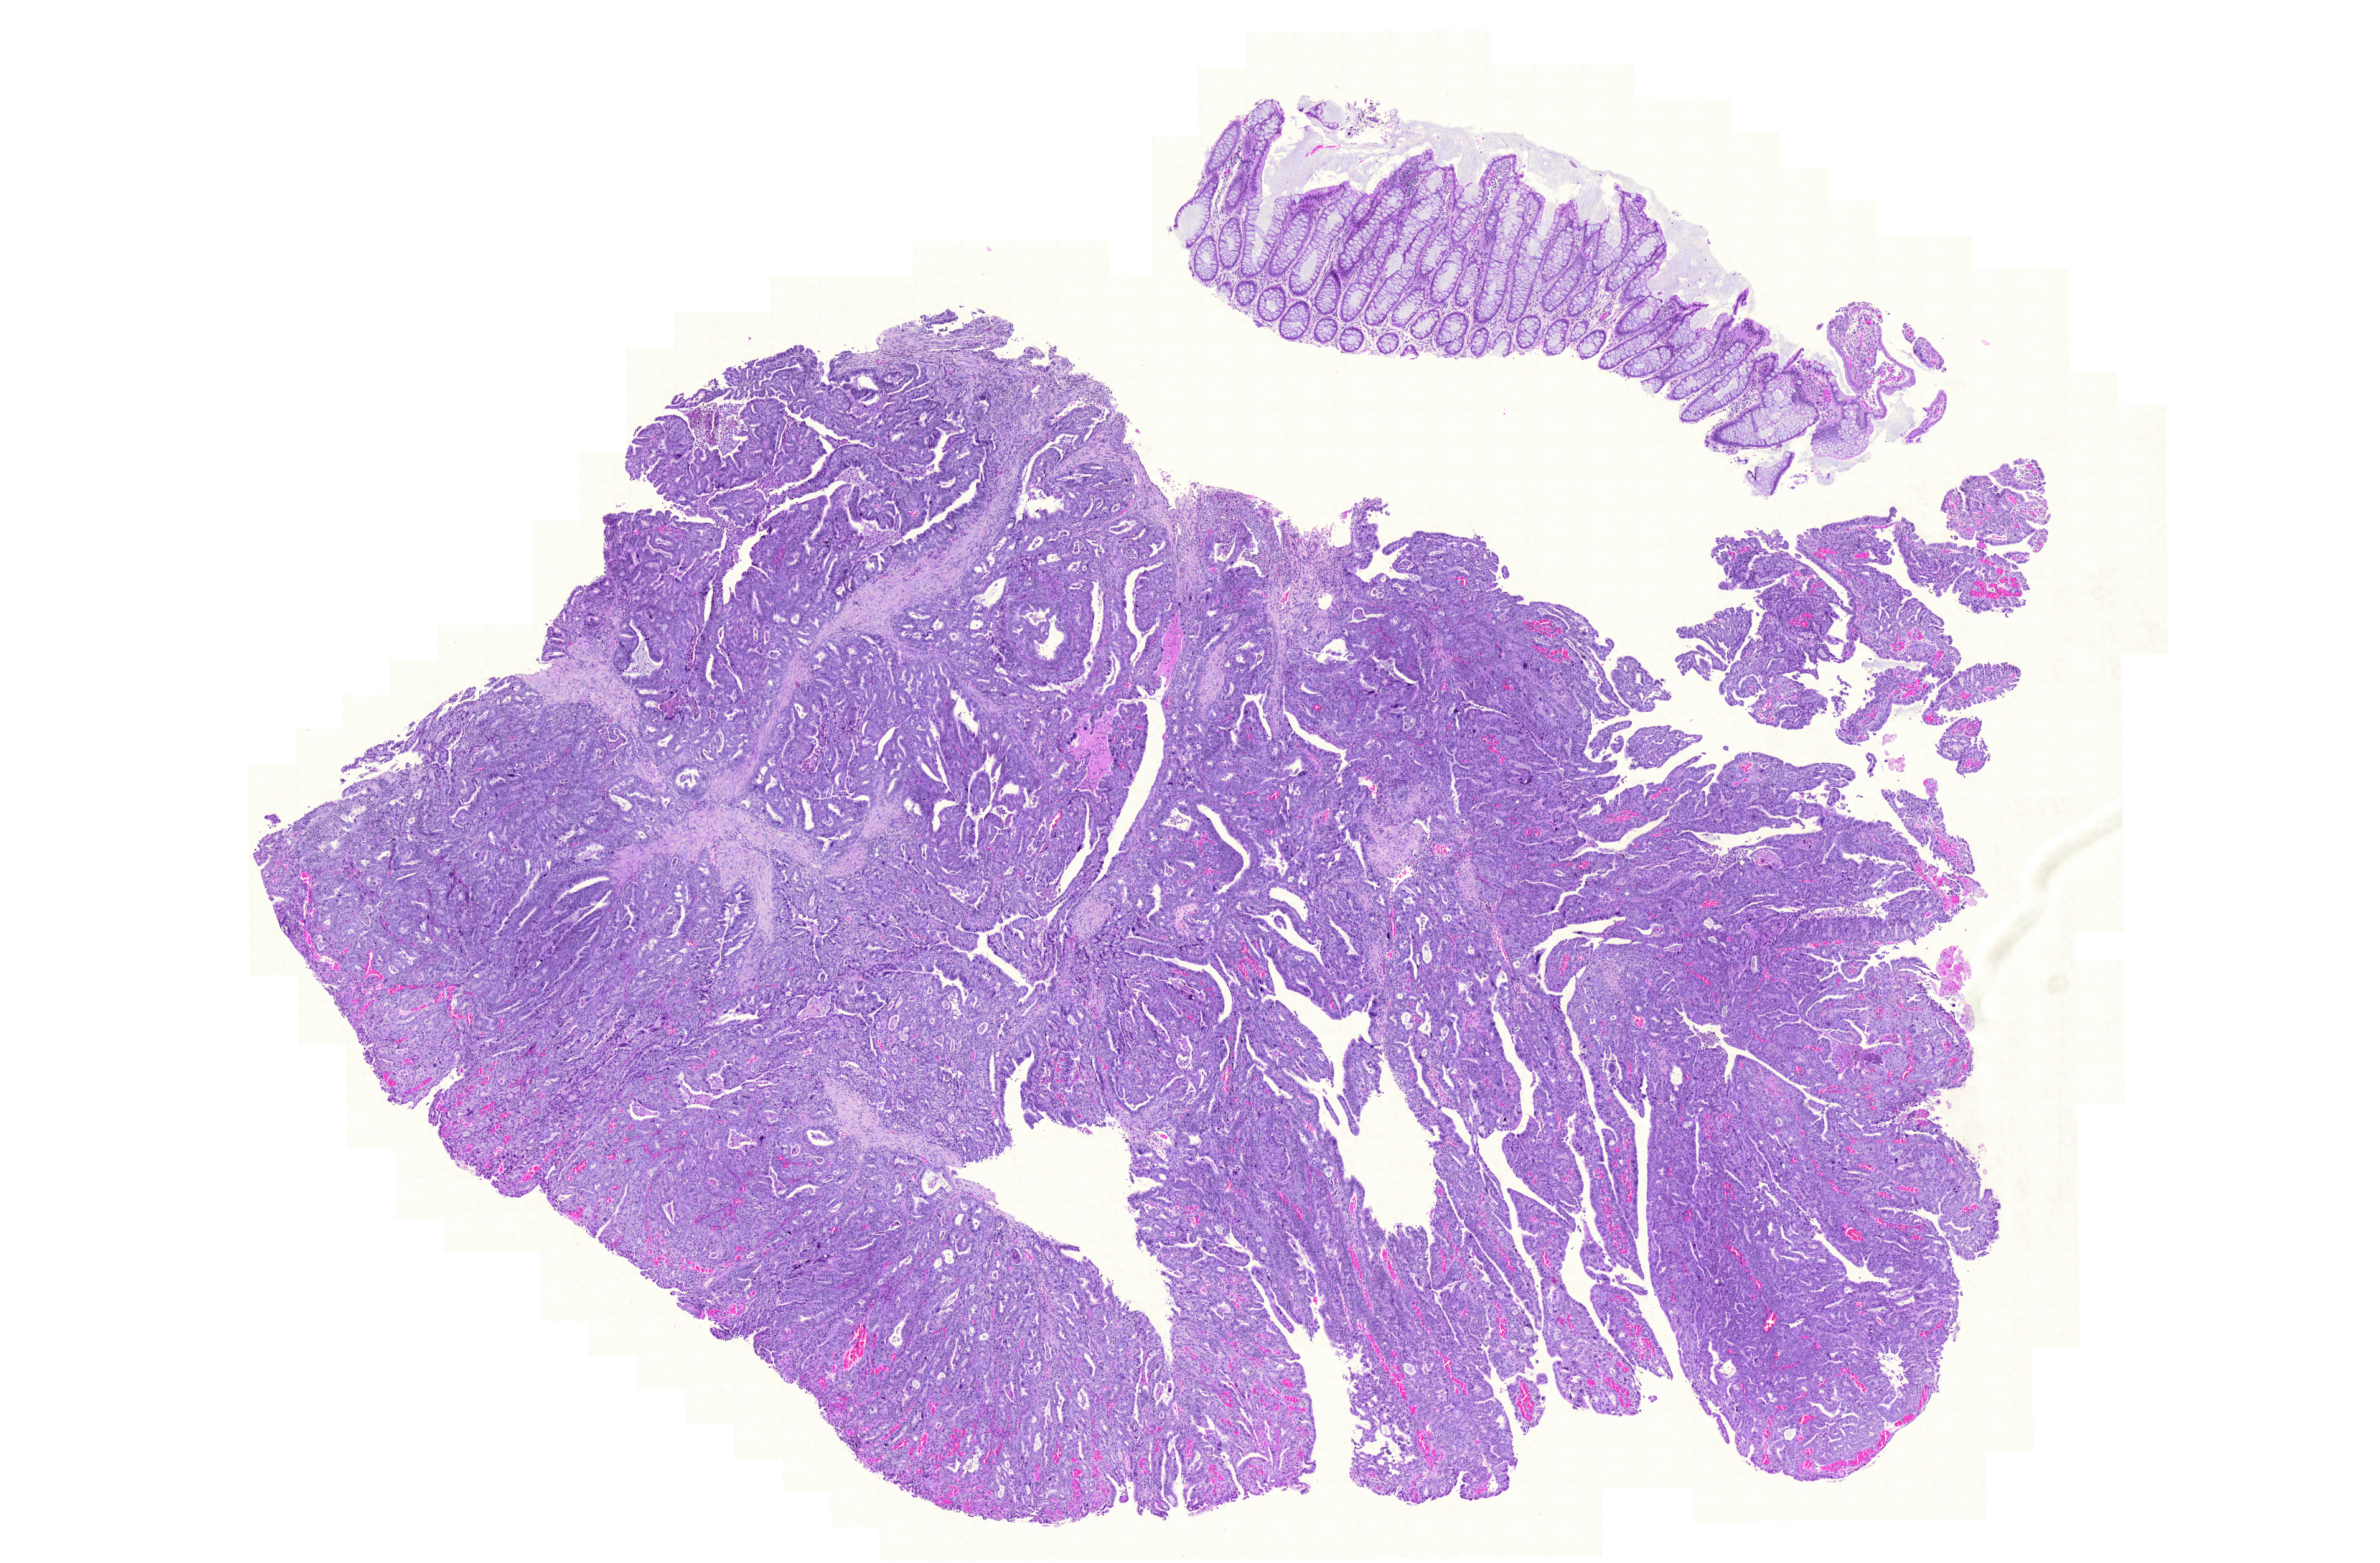
Digitized Hematoxylin and eosin (H&E) stained tissue section (whole slide), low-resolution overview of the scanned area, about 14.2 x 9.3 mm (slide scanned at 20x); formalin-fixed paraffin-embedded (FFPE) diagnostic section; rectum, primary tumour sample. Male patient; age at initial diagnosis 35 years.
* AJCC pathologic stage: I
* lymph nodes positive (case pathology): 0 of 34 examined
* TNM: T2 N0 M0
* histologic diagnosis: Adenocarcinoma, NOS